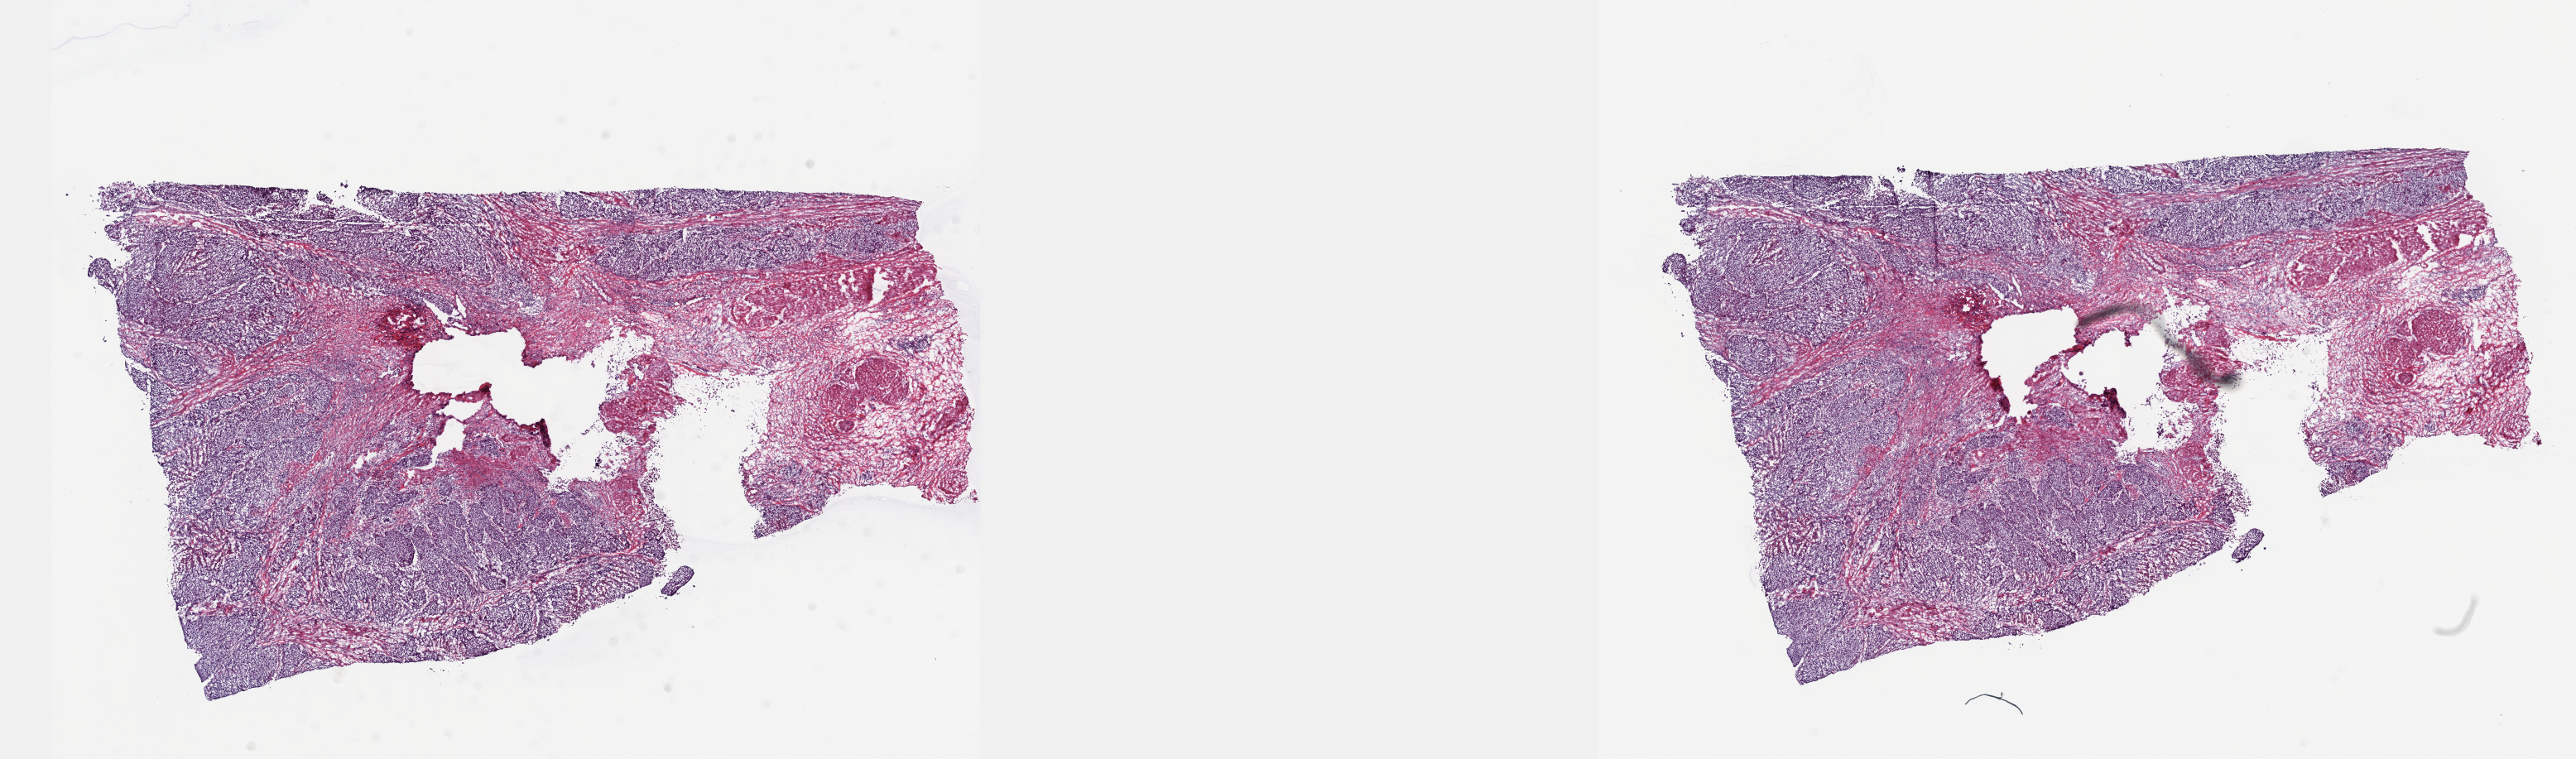
H&E-stained whole-slide image, a low-resolution overview of the entire scanned area, about 25.1 x 7.4 mm (slide scanned at 40x), frozen section, primary tumour sample from the bladder. Male patient; age at initial diagnosis 64 years. Histologic grade: high grade. Composition of this section per pathologist review: tumour cells 60%, tumour nuclei 70%, normal cells 20%, stromal cells 20%, necrosis 0%. Infiltration values recorded for this section: lymphocyte infiltration 0%, monocyte infiltration 0%, neutrophil infiltration 0%.
AJCC pathologic stage: III. Histologic diagnosis: Transitional cell carcinoma. Lymph nodes positive (case pathology): 0 of 17 examined.